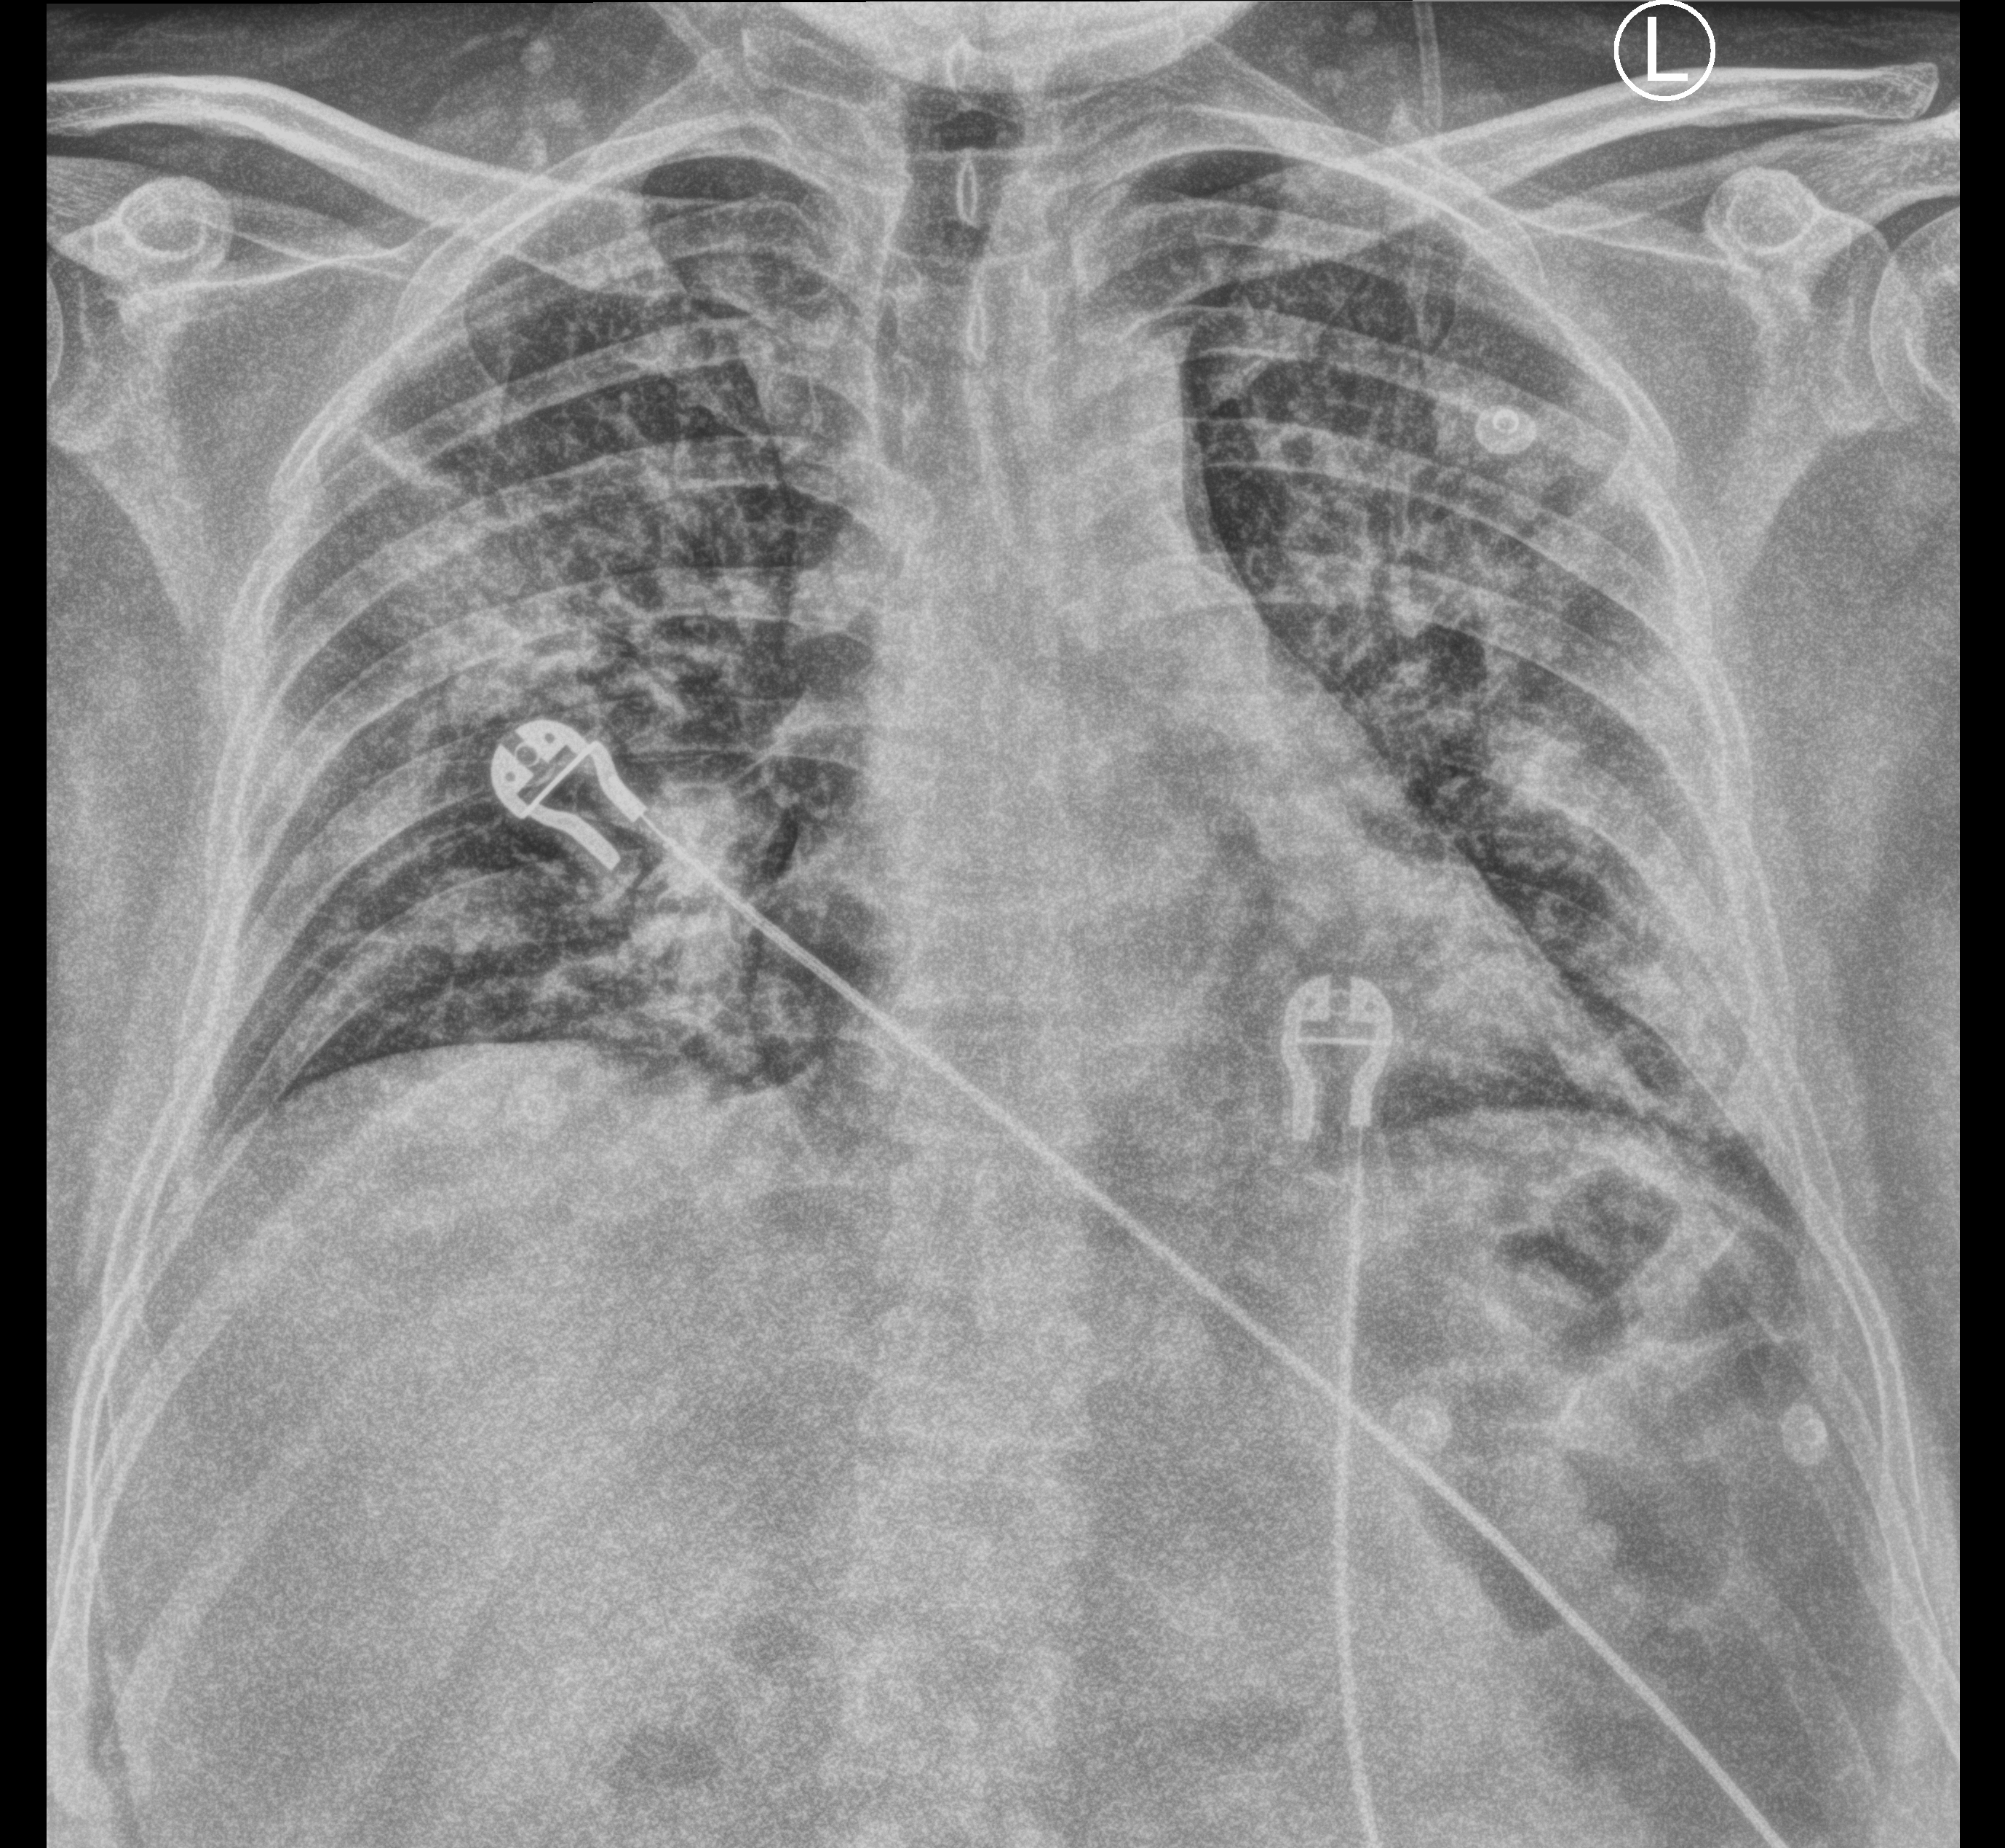
Chest X-ray (portable), anteroposterior (AP) projection. Patient hospitalised with COVID-19; male, aged 18–59 years.
Hospital-stay facts (about this admission, not read from this image; timing relative to this image not recorded): length of hospital stay: 9 days; admitted to intensive care during this hospital stay: no.